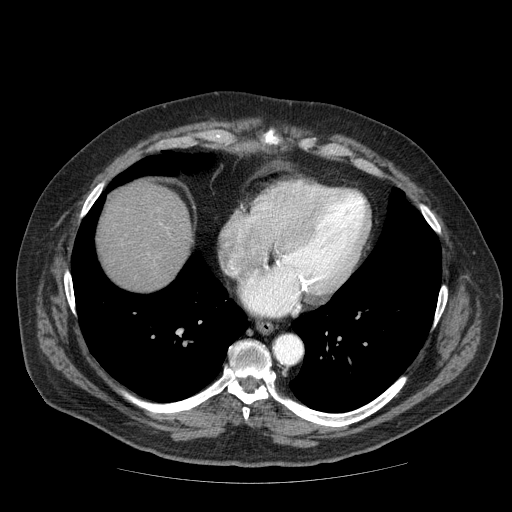
Contrast-enhanced abdominal CT (liver protocol), one axial slice. Slice 69 of 85 in the series (ordered by position). Reconstruction kernel STANDARD. 120 kVp. Soft-tissue window (W 400 / L 40 HU). 2.5 mm slice thickness. 512 × 512 image matrix. From the clinical record (not read from this slice): diagnosis: hepatocellular carcinoma (patient treated with transarterial chemoembolisation; whether this scan precedes or follows treatment is not stated here); TNM stage (as recorded): Stage-IIIA; Child-Pugh class: A; tumour size: 7 cm.
Outlined on this slice (semi-automatic segmentation, software-assisted and operator-edited):
- liver parenchyma outside the tumour (the mass and vessels are separate outlines, so this box may not span the whole liver): box from (x=98, y=182) to (x=192, y=290) px